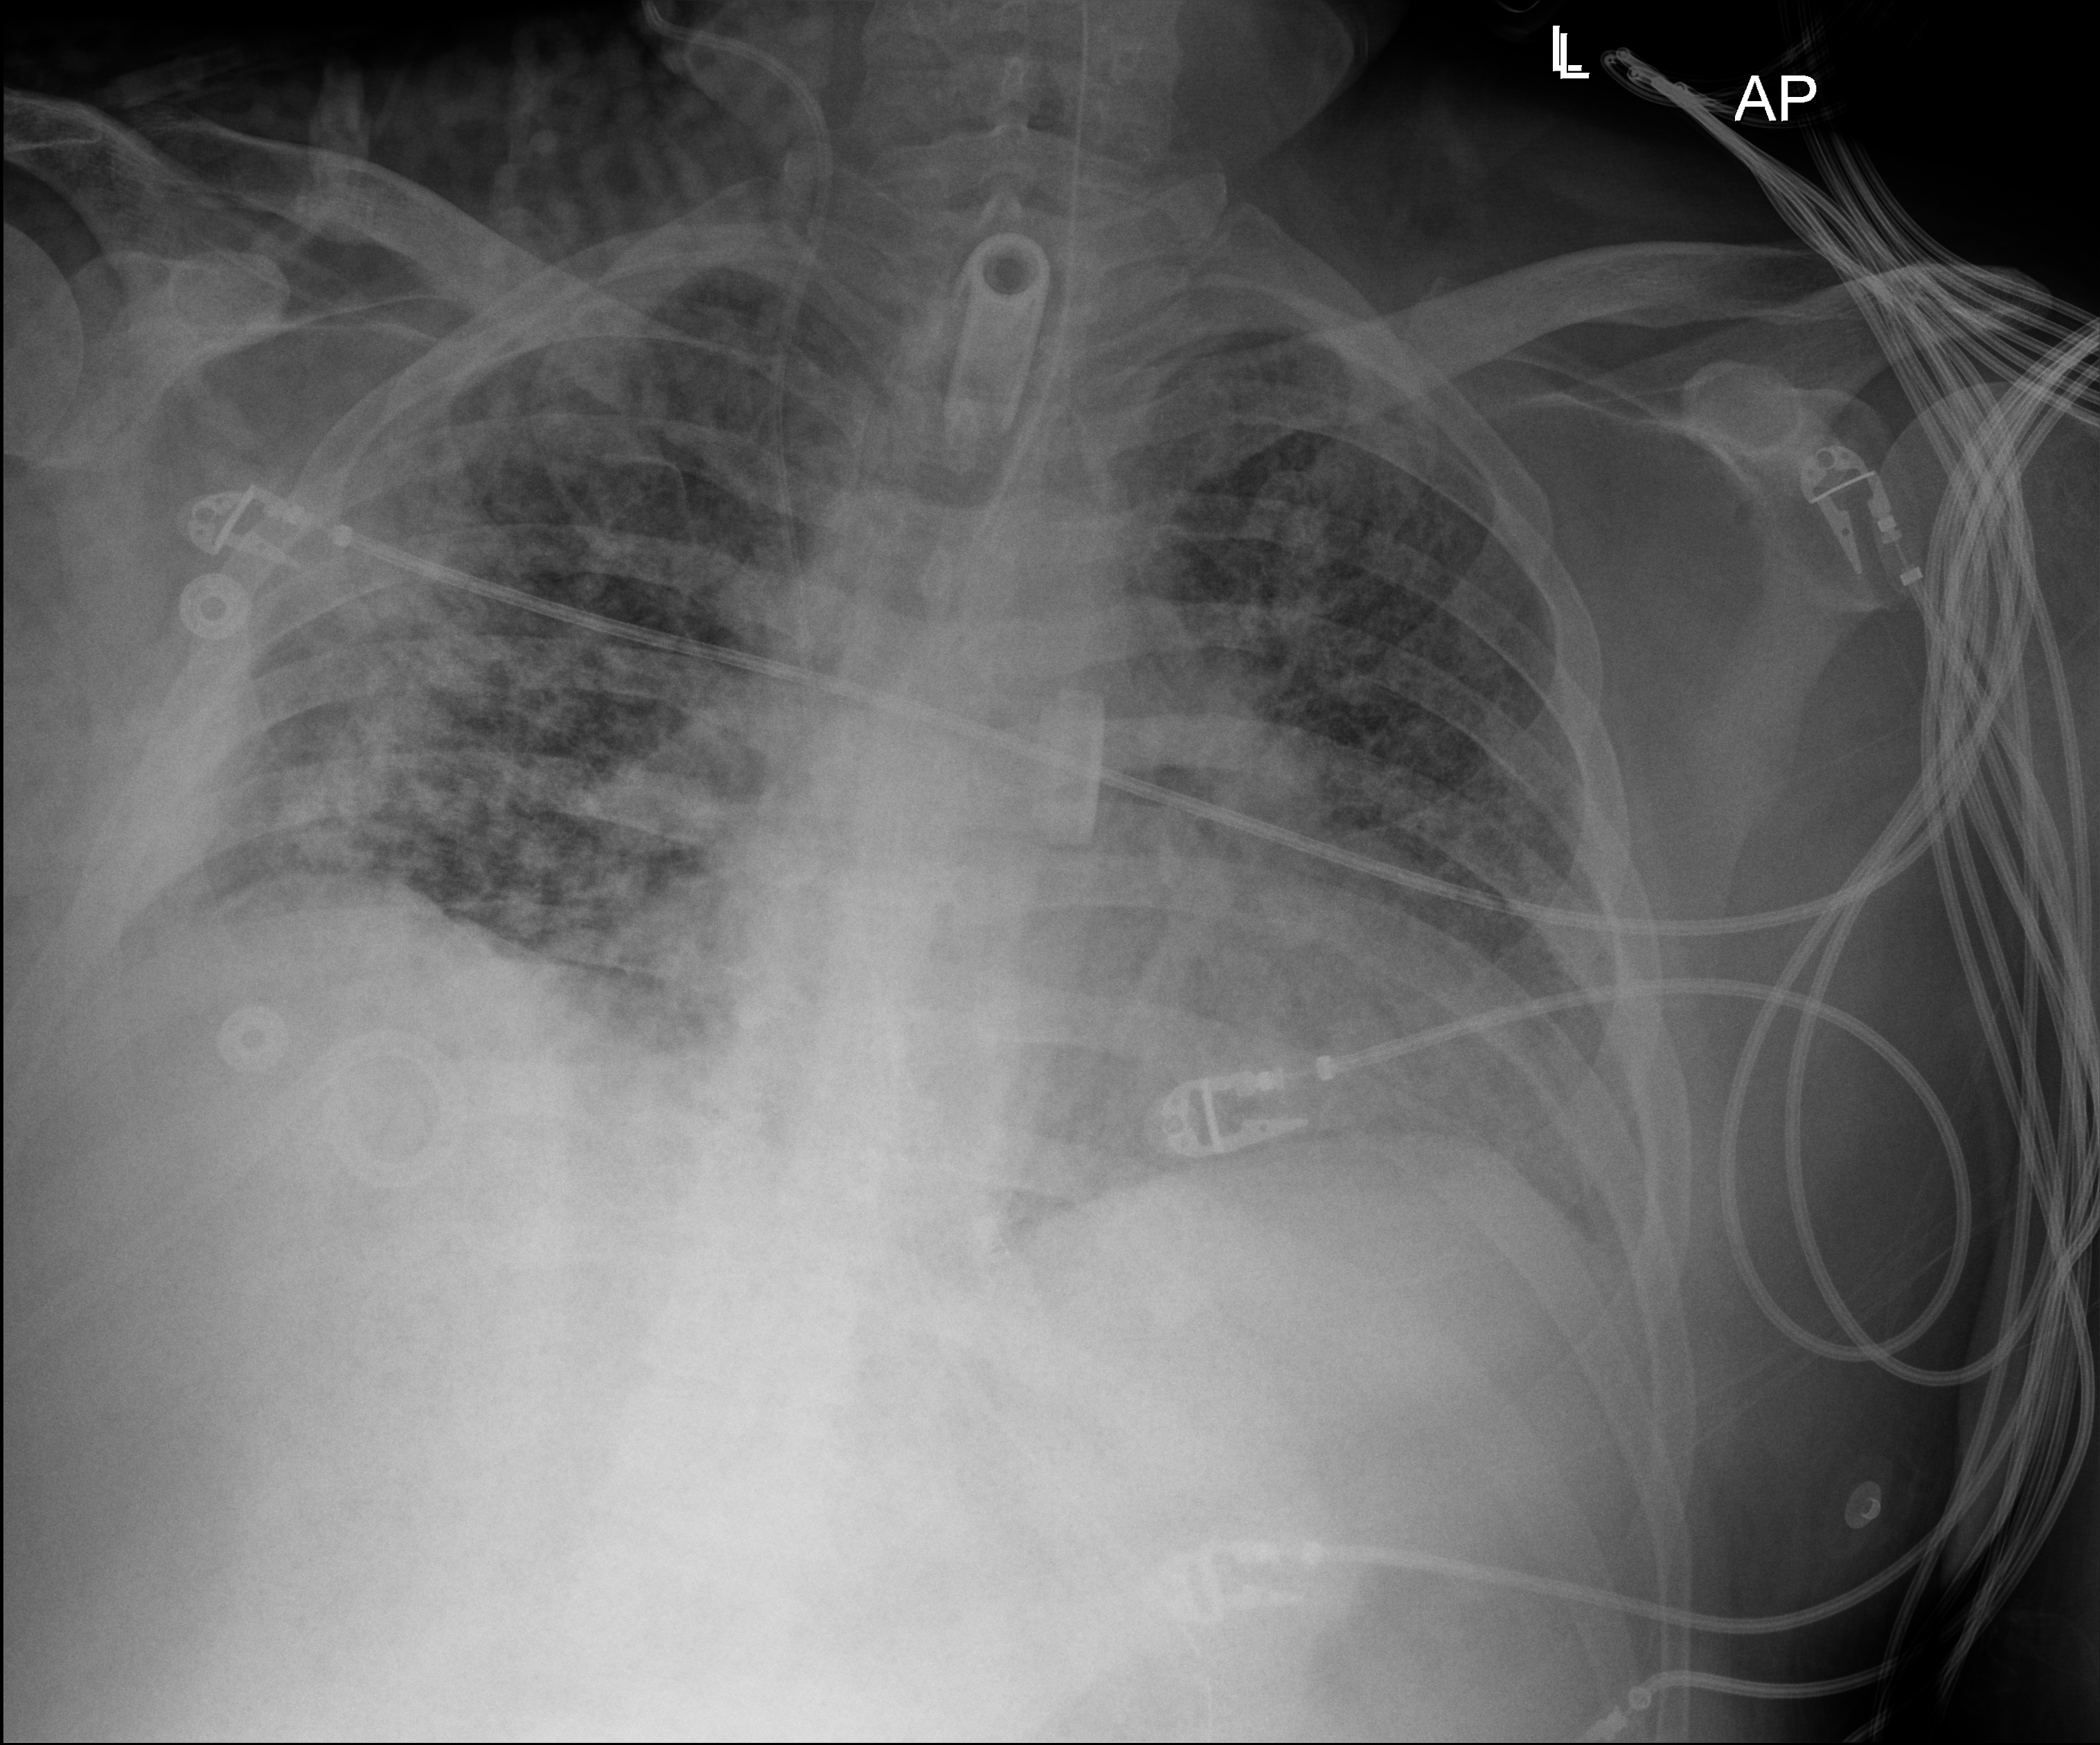
Chest X-ray (portable); anteroposterior (AP) projection. Male patient hospitalised with COVID-19, age 18–59 years.
From the hospital-stay record, not from the radiograph (when in the stay this image was taken is not recorded):
- diabetes (admission record): no
- smoking status (admission record): never
- admitted to intensive care during this hospital stay: yes